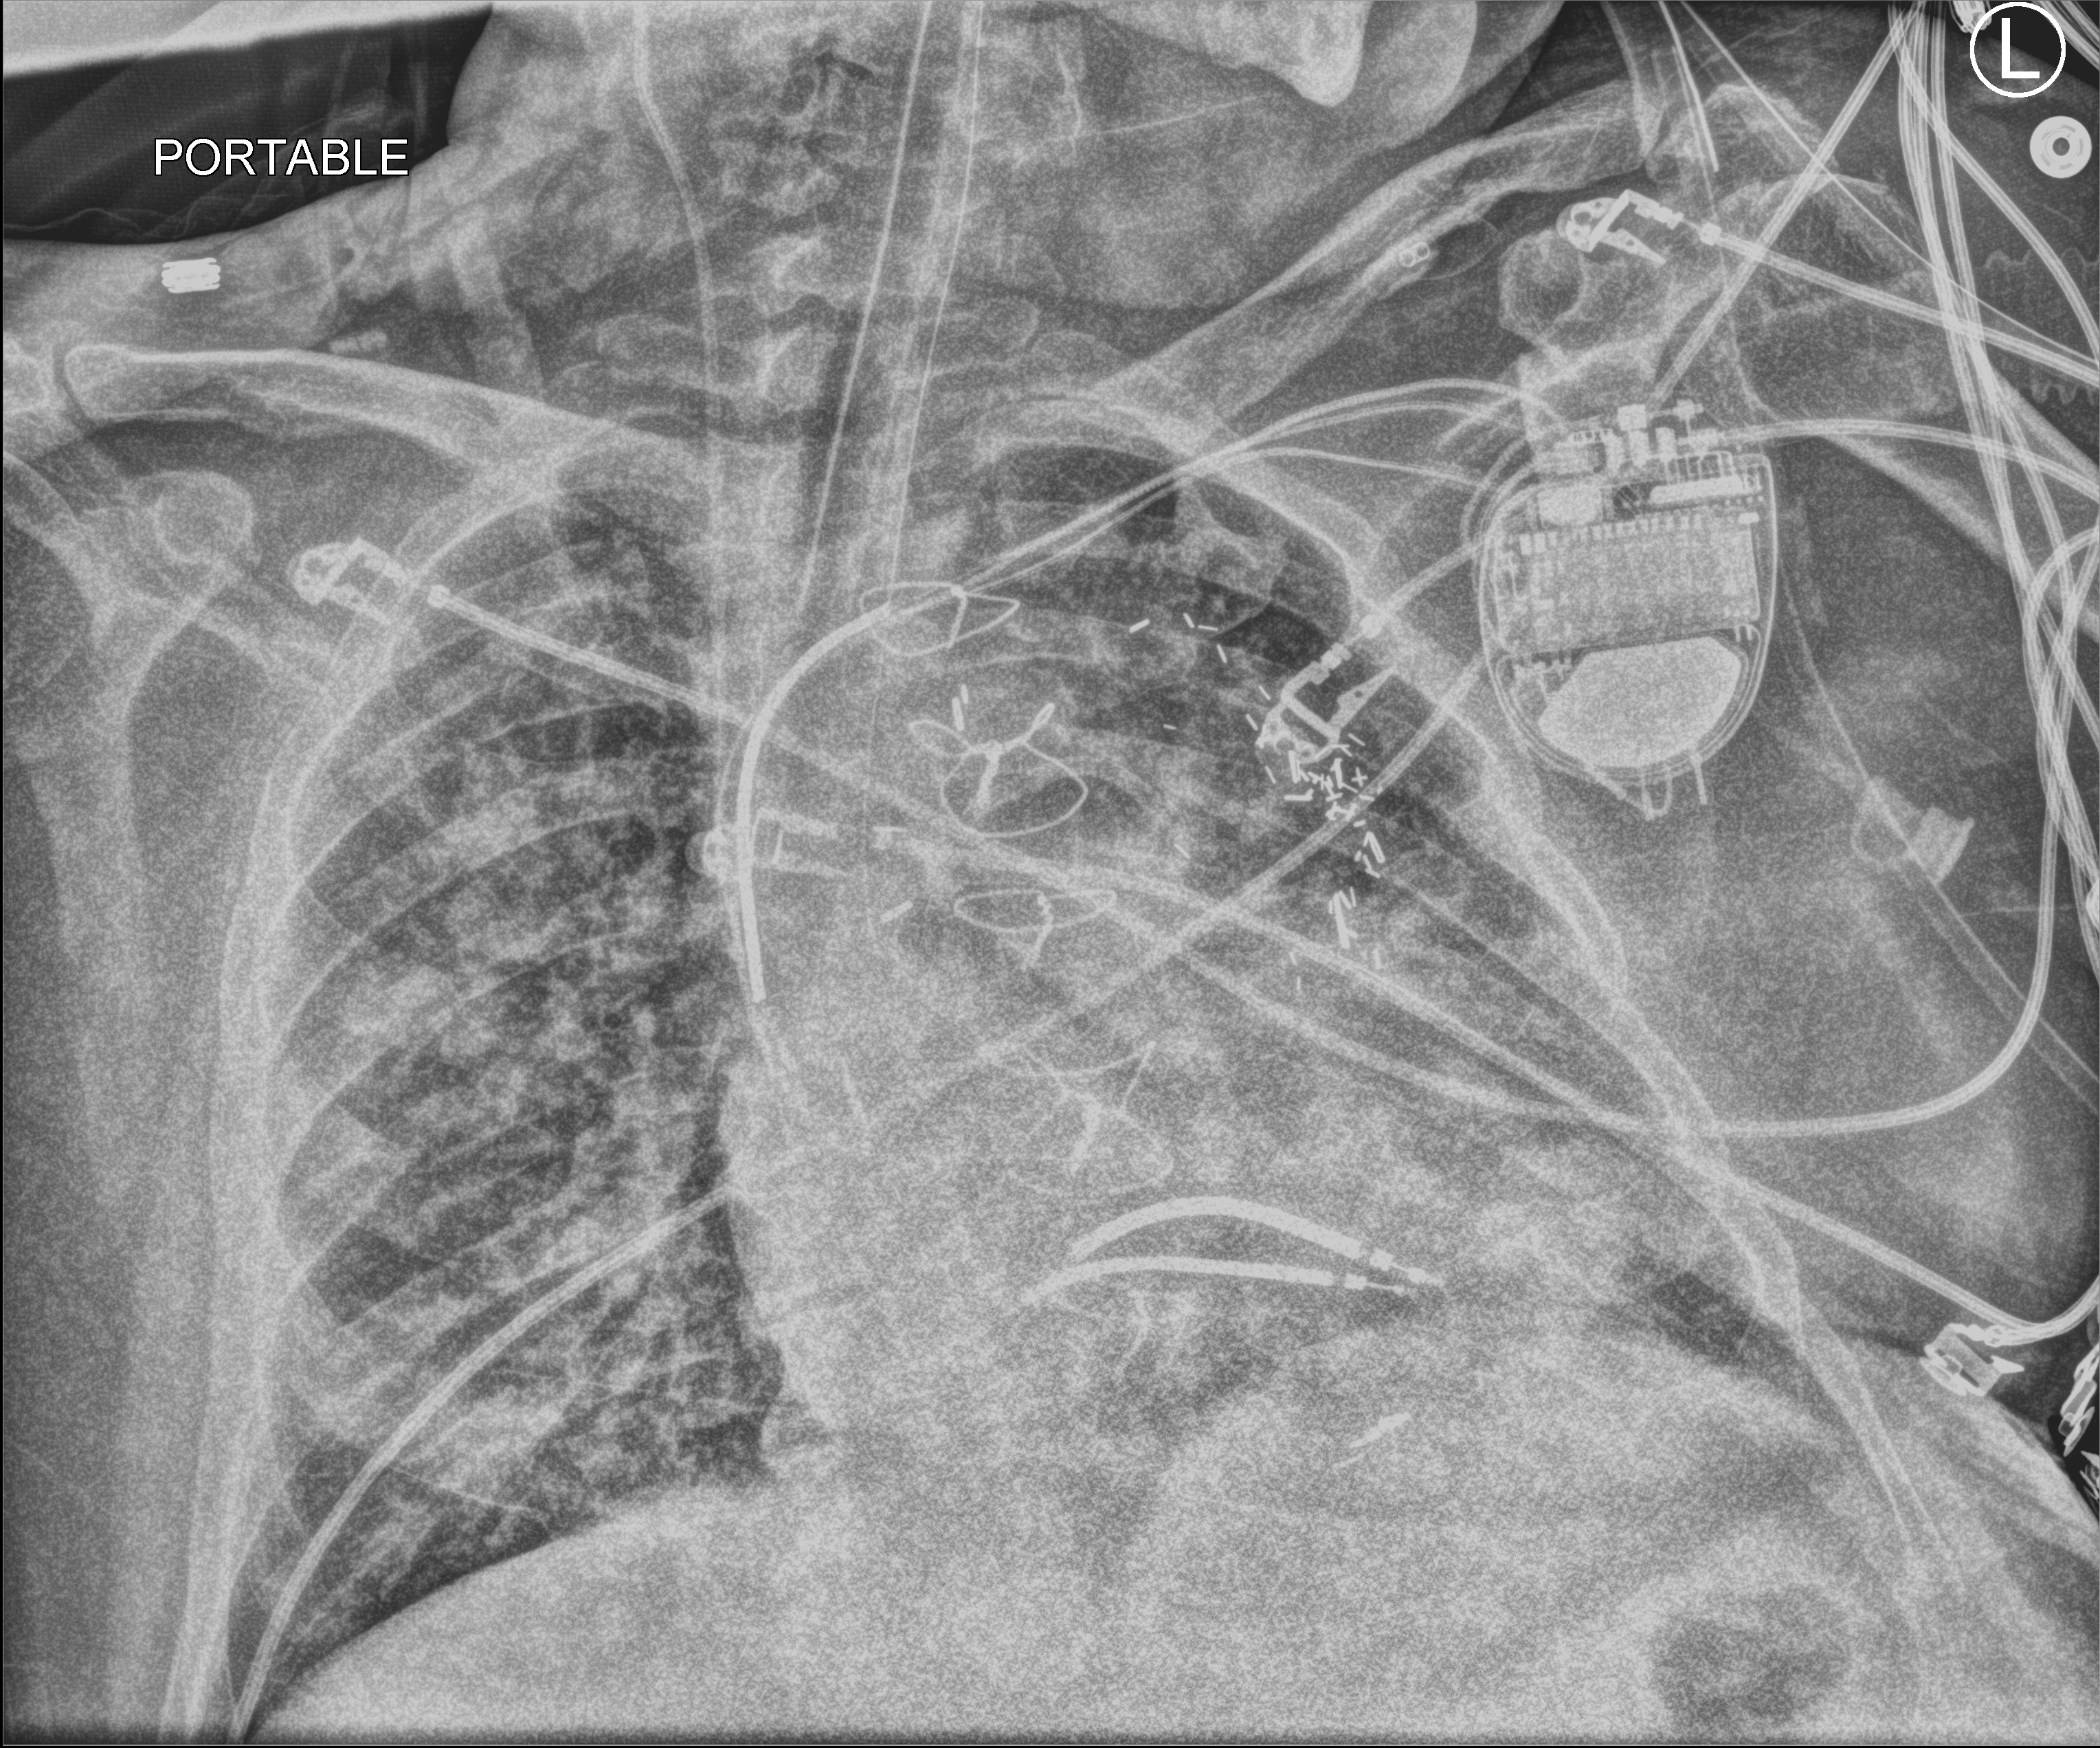
Bedside chest radiograph (computed radiography). Patient hospitalised with COVID-19; male, aged 60–74 years.
From the hospital-stay record, not from the radiograph (when in the stay this image was taken is not recorded): COPD (admission record): no; hypertension (admission record): yes.